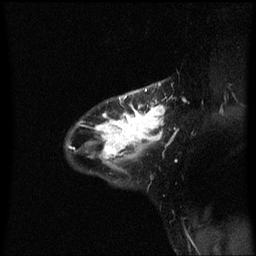
Breast MRI (dynamic contrast-enhanced), one sagittal slice; slice 44 of 60 in the series (ordered by position); dynamic contrast-enhanced series, image 2 of 3 at this slice position (ordered by acquisition); 1.5 T; TE 4.2 ms, TR 8.4 ms; 256 × 256 image matrix. Patient: female, 32 years.
Structures marked on this image (semi-automatic segmentation, software-assisted and operator-edited):
- analysis volume of interest (the breast-tissue region the enhancement analysis was run in; not a lesion): box from (x=67, y=82) to (x=167, y=167) px
- tumour enhancement mask (voxels above the 70 % enhancement threshold inside the analysis volume of interest): (x=70, y=84)–(x=166, y=159)